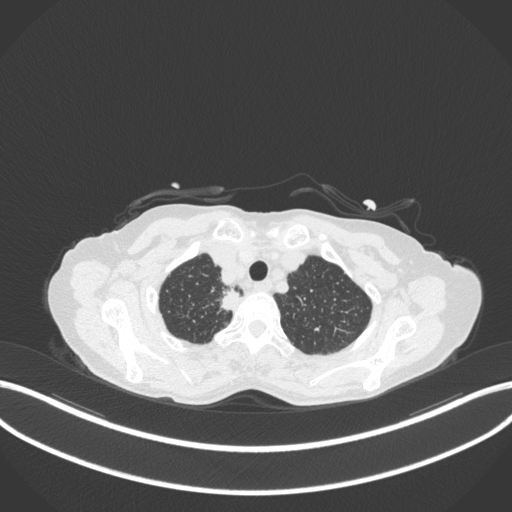
Chest CT, one axial slice; slice 328 of 363 in the series (ordered by position); reconstruction kernel B31f; 120 kVp; lung window (W 1500 / L -600 HU); 1 mm slice thickness; 512 × 512 image matrix, field of view 400 × 400 mm. Patient: female, 75 years. Case-level facts recorded for this patient, not image findings: clinical TNM (as recorded): T1c N1 M1.
Outlined on this slice (bounding box drawn by a radiologist):
- lung tumour (recorded histology: adenocarcinoma): bounding box [x1, y1, x2, y2] px = [215, 286, 244, 315]